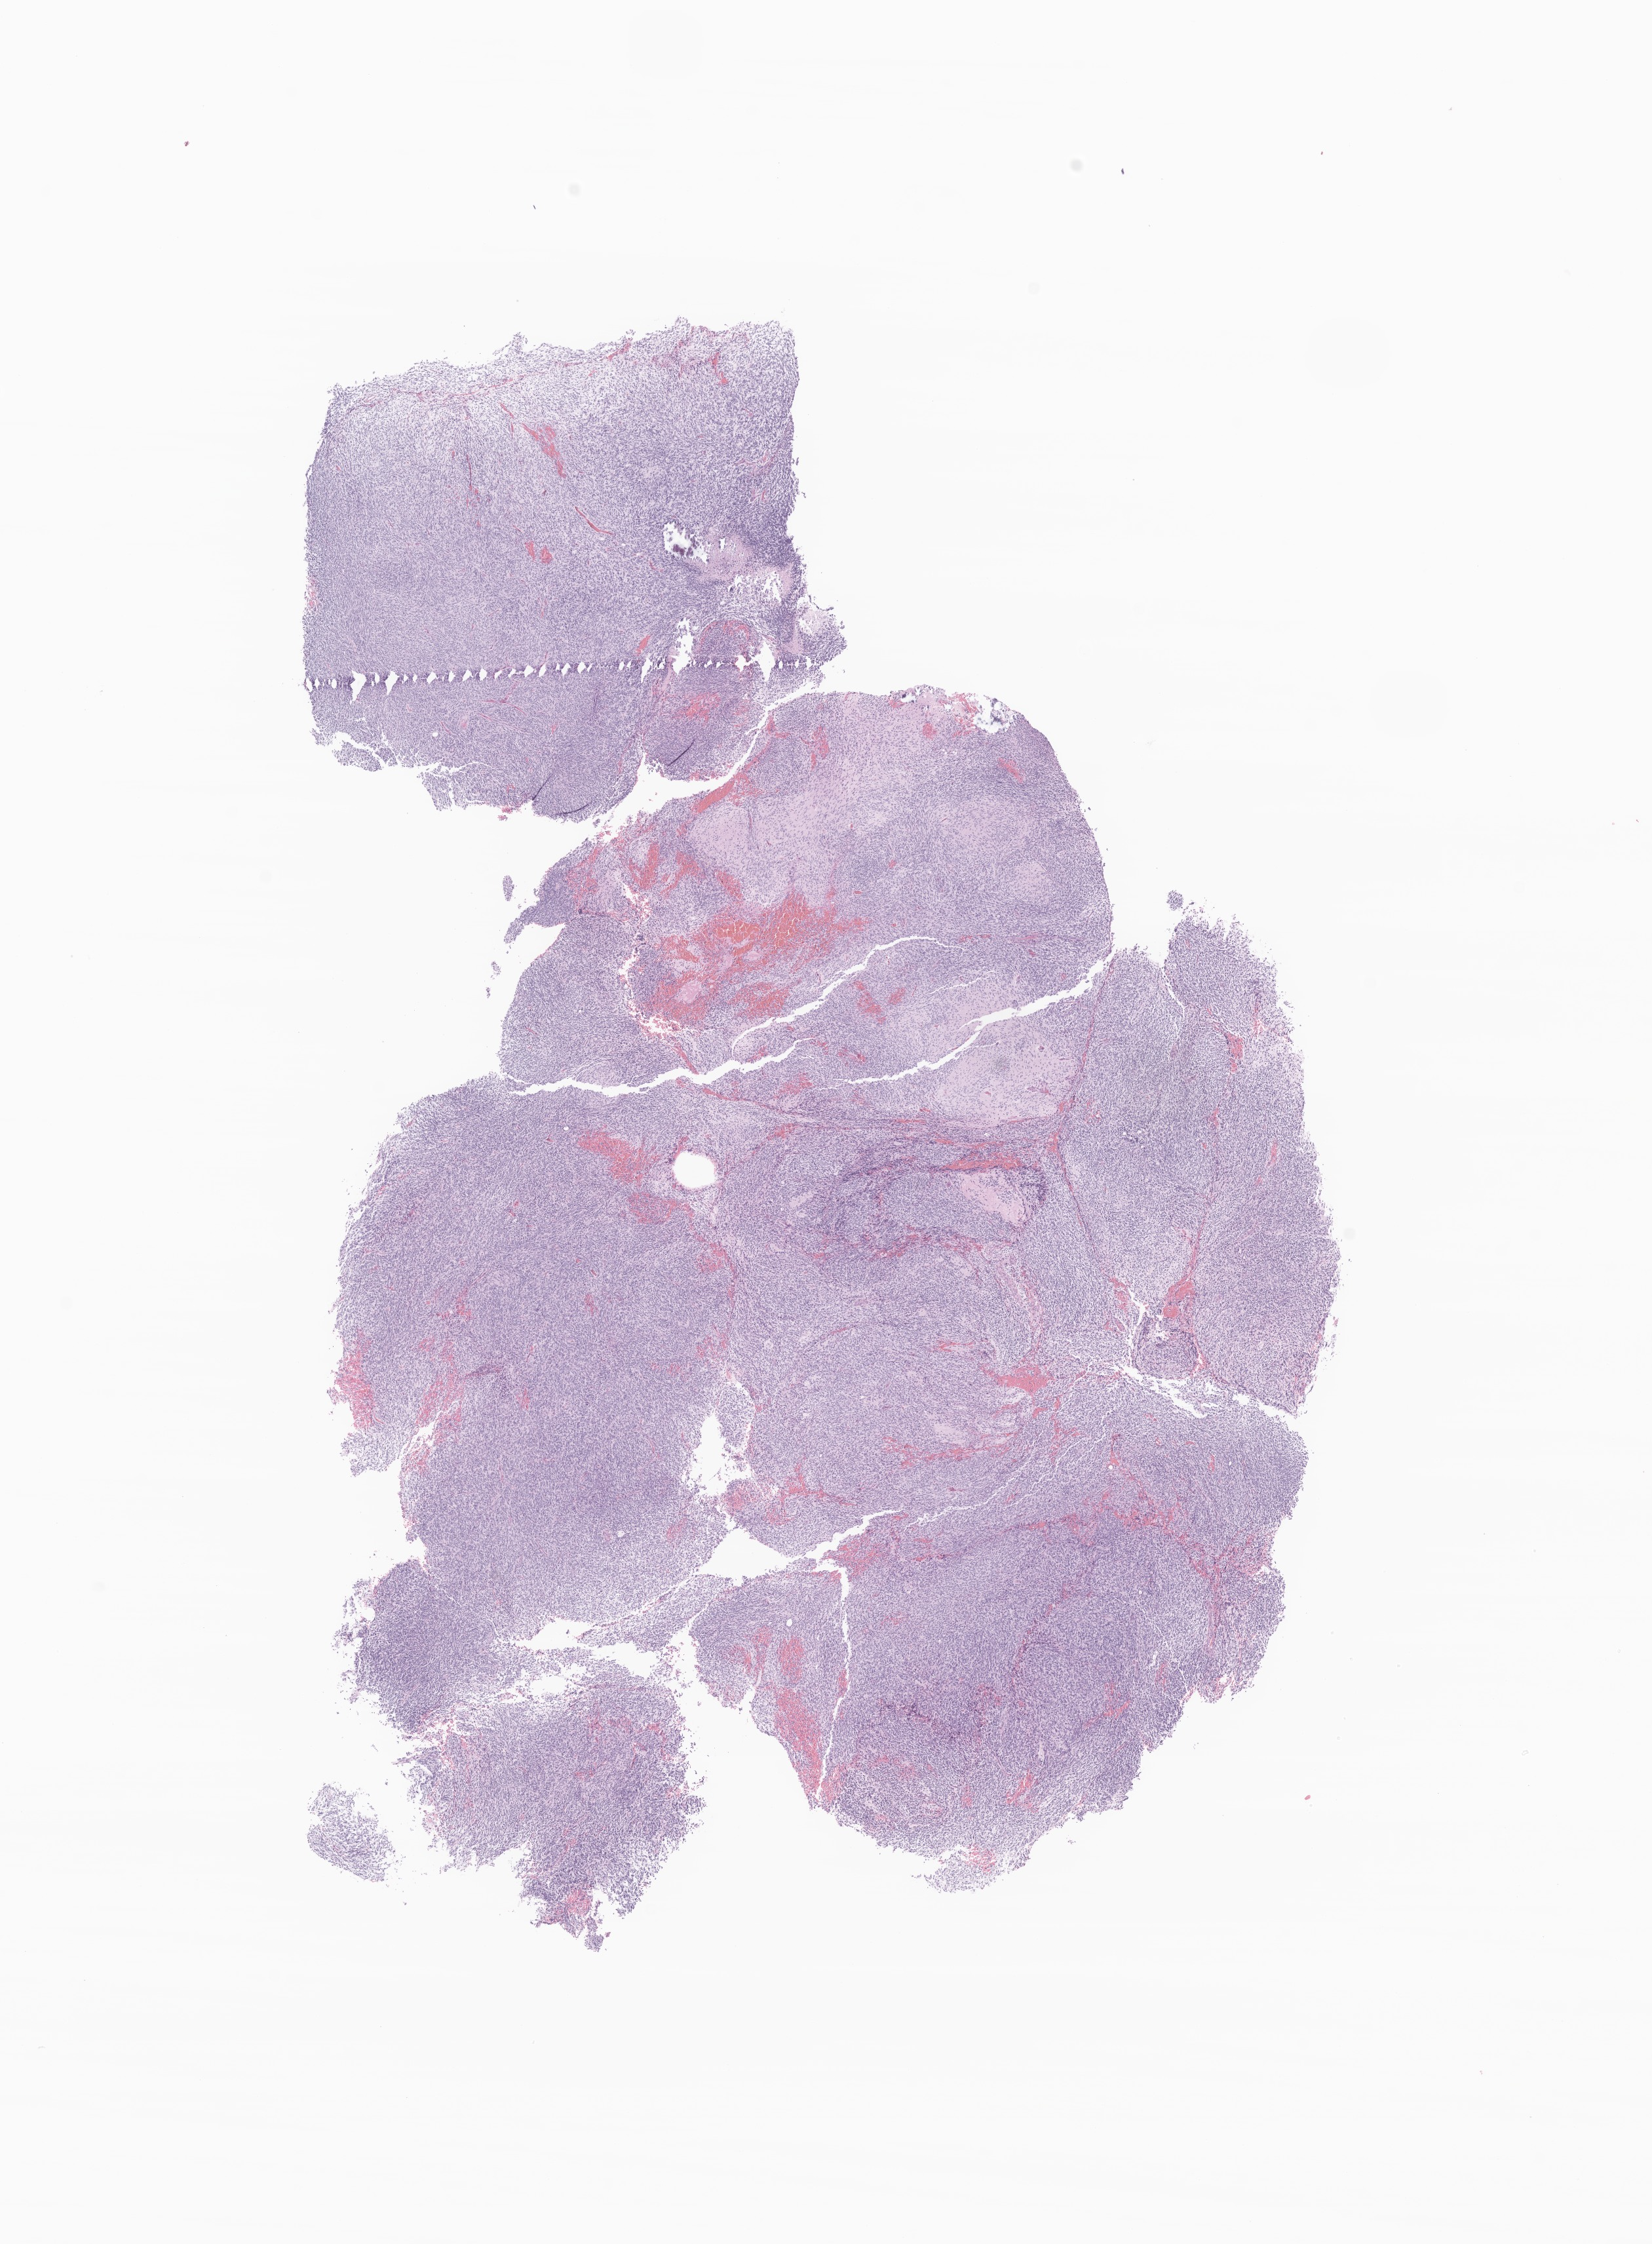
Whole-slide image, hematoxylin and eosin (H&E) stain of tumor tissue from the cerebellum, whole scanned area (about 10.6 x 14.4 mm) shown as a low-resolution overview; formalin-fixed, paraffin-embedded (FFPE) tissue. Patient male; age 148 months (12 years 4 months).
Diagnosis (ICD-O-3 morphology term): Medulloblastoma, NOS.